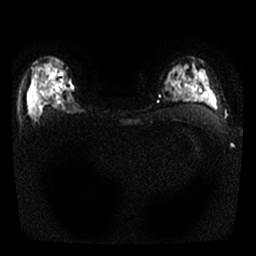
Breast MRI, one axial slice; slice 19 of 25 in the series (ordered by position); diffusion-weighted series; image 2 of 4 stored at this slice position (different b-values; order by instance number); 1.5 T; 256 × 256 image matrix, field of view 300 × 300 mm. Female patient.
Structures marked on this image (manually delineated by an expert):
- tumour on diffusion-weighted imaging: bounding box [x1, y1, x2, y2] px = [29, 66, 78, 118]